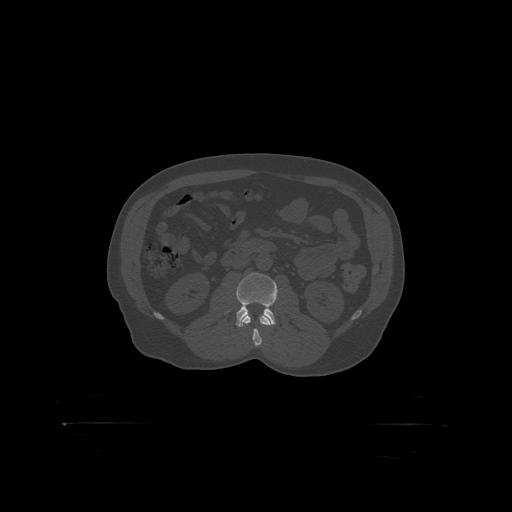
CT including the spine, one axial slice. Position 279 of 399 along the scan axis. Reconstruction kernel STANDARD. Bone window (W 1800 / L 400 HU). 1.25 mm slice thickness. 512 × 512 image matrix. Male patient, age 46 years. Case-level facts recorded for this patient, not image findings: primary cancer: skin.
Annotated regions visible in this slice (semi-automatically segmented with operator editing):
- L2 vertebra: bounding box (x1, y1, x2, y2) in pixels: (244, 315, 266, 319)
- L3 vertebra: (229, 273, 278, 319)